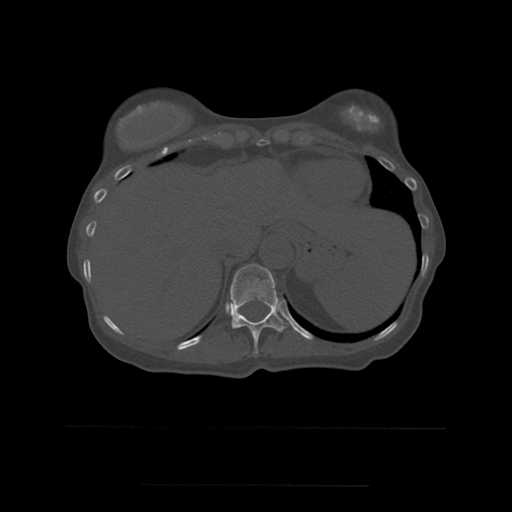
CT including the spine, one axial slice. Slice 281 of 544 in the series (ordered by position). Bone window (W 1800 / L 400 HU). 512 × 512 image matrix. Patient age 58 years. From the clinical record (not read from this slice): primary cancer: lung.
Annotated regions visible in this slice (semi-automatically segmented with operator editing):
- T11 vertebra: bounding box [x1, y1, x2, y2] px = [230, 264, 287, 354]